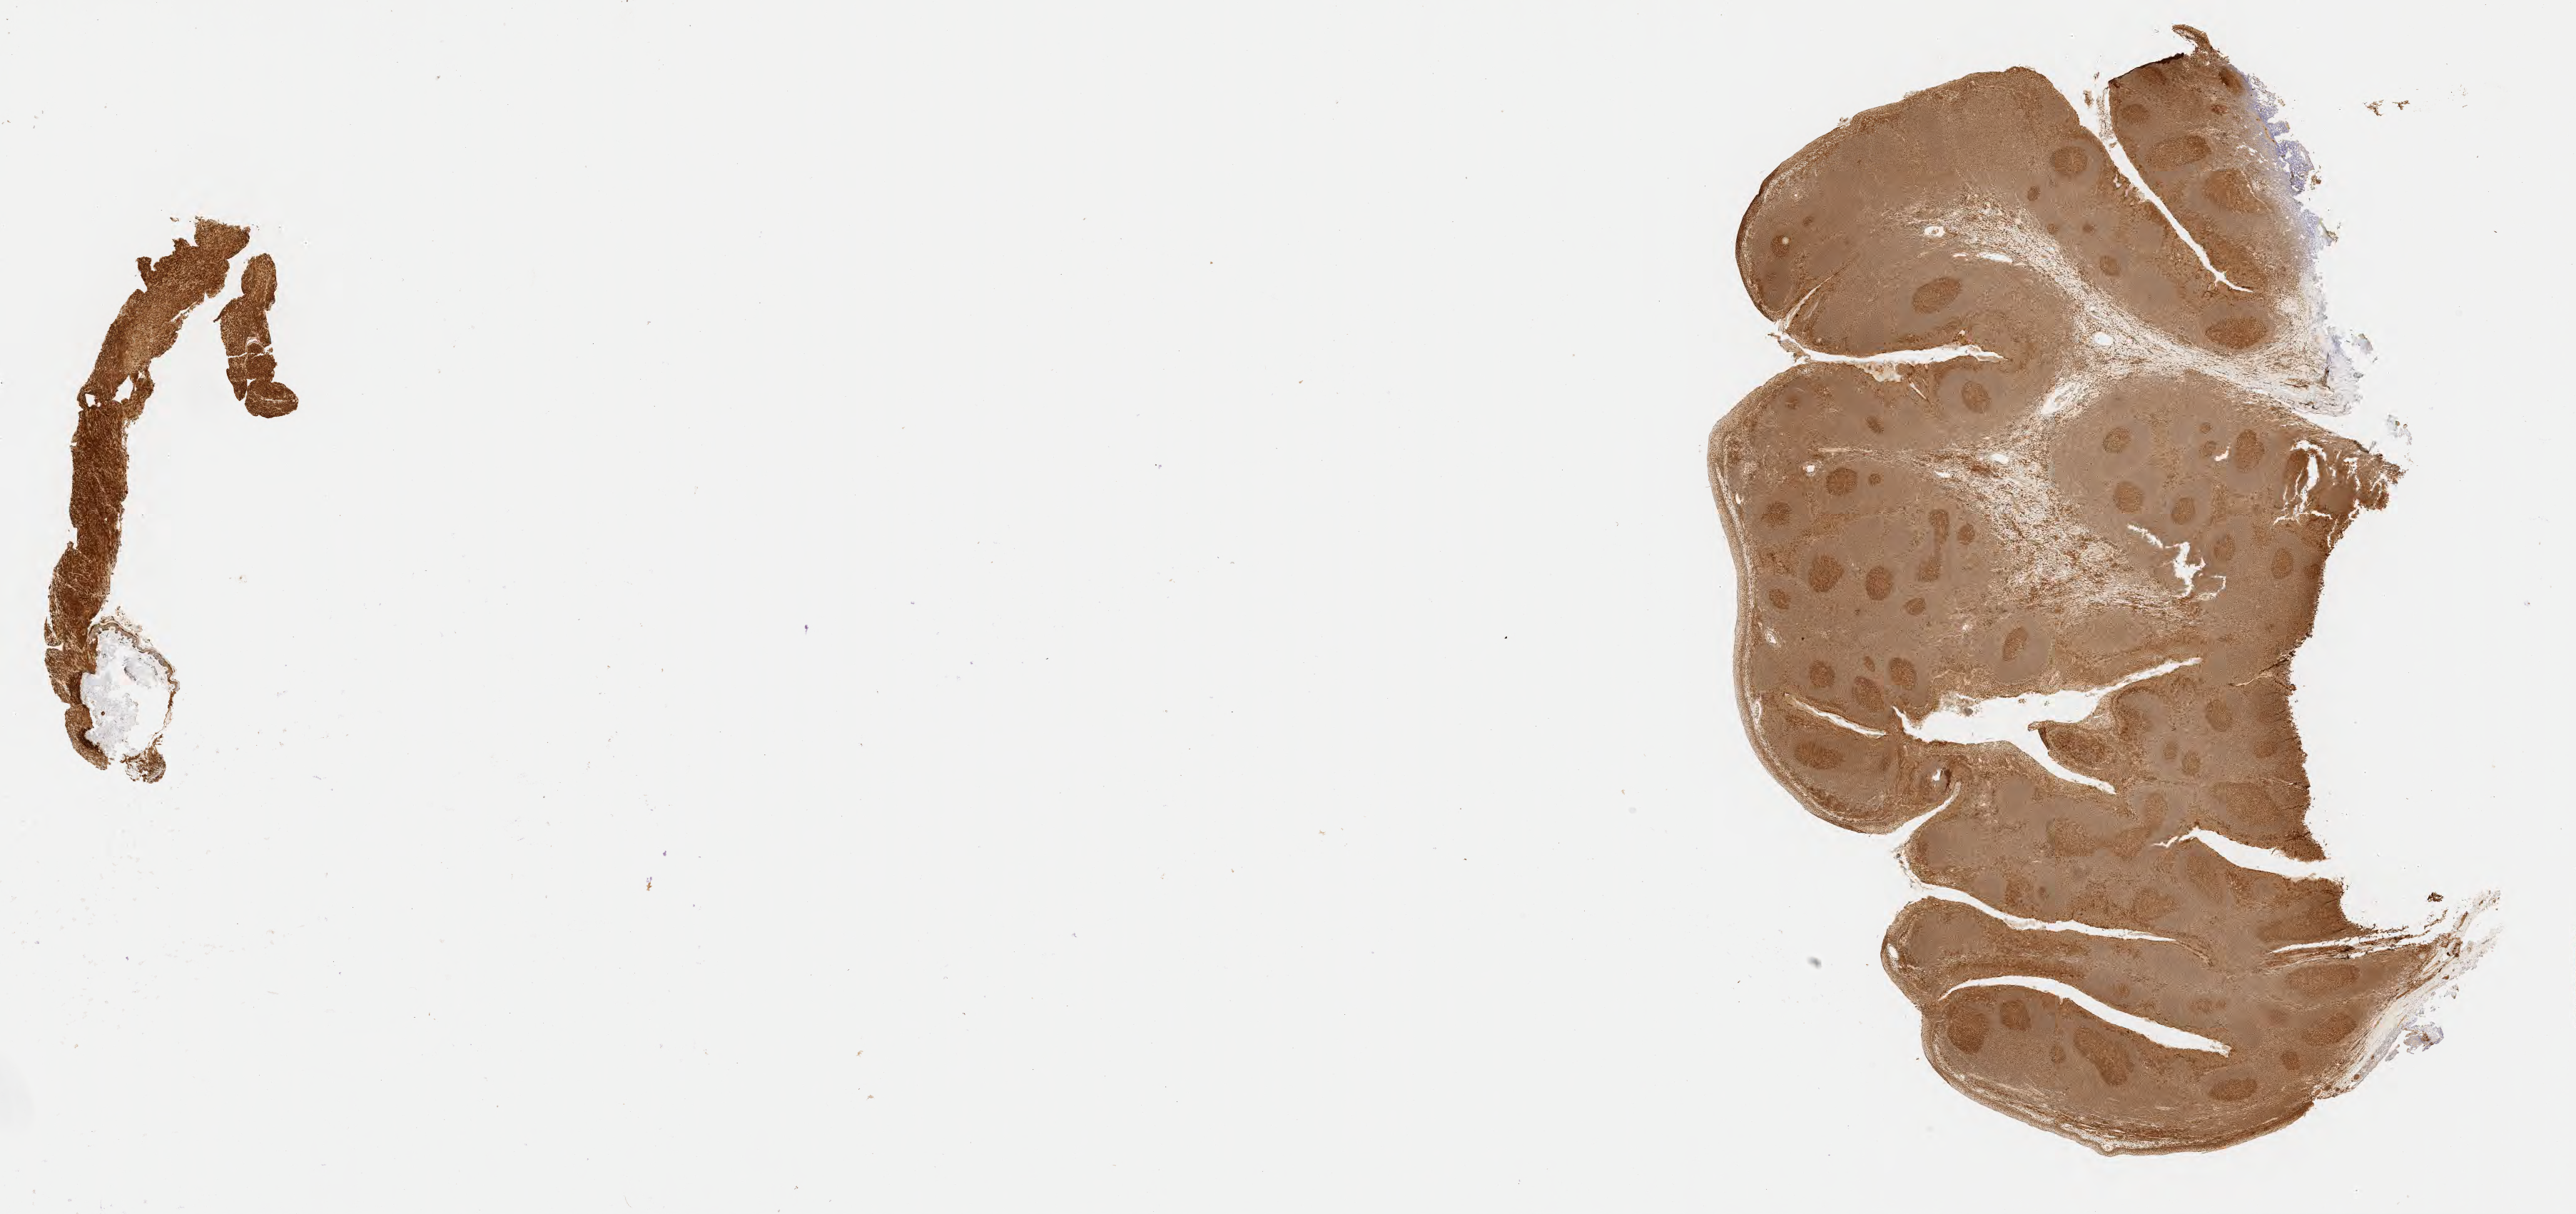
Immunohistochemistry (IHC) whole-slide image stained for BCL6, shown as a low-resolution overview of the whole scanned area (about 29.2 x 13.8 mm), tumor tissue. Patient: female, 43 years old.
Histologic diagnosis: Diffuse large B-cell lymphoma, NOS.